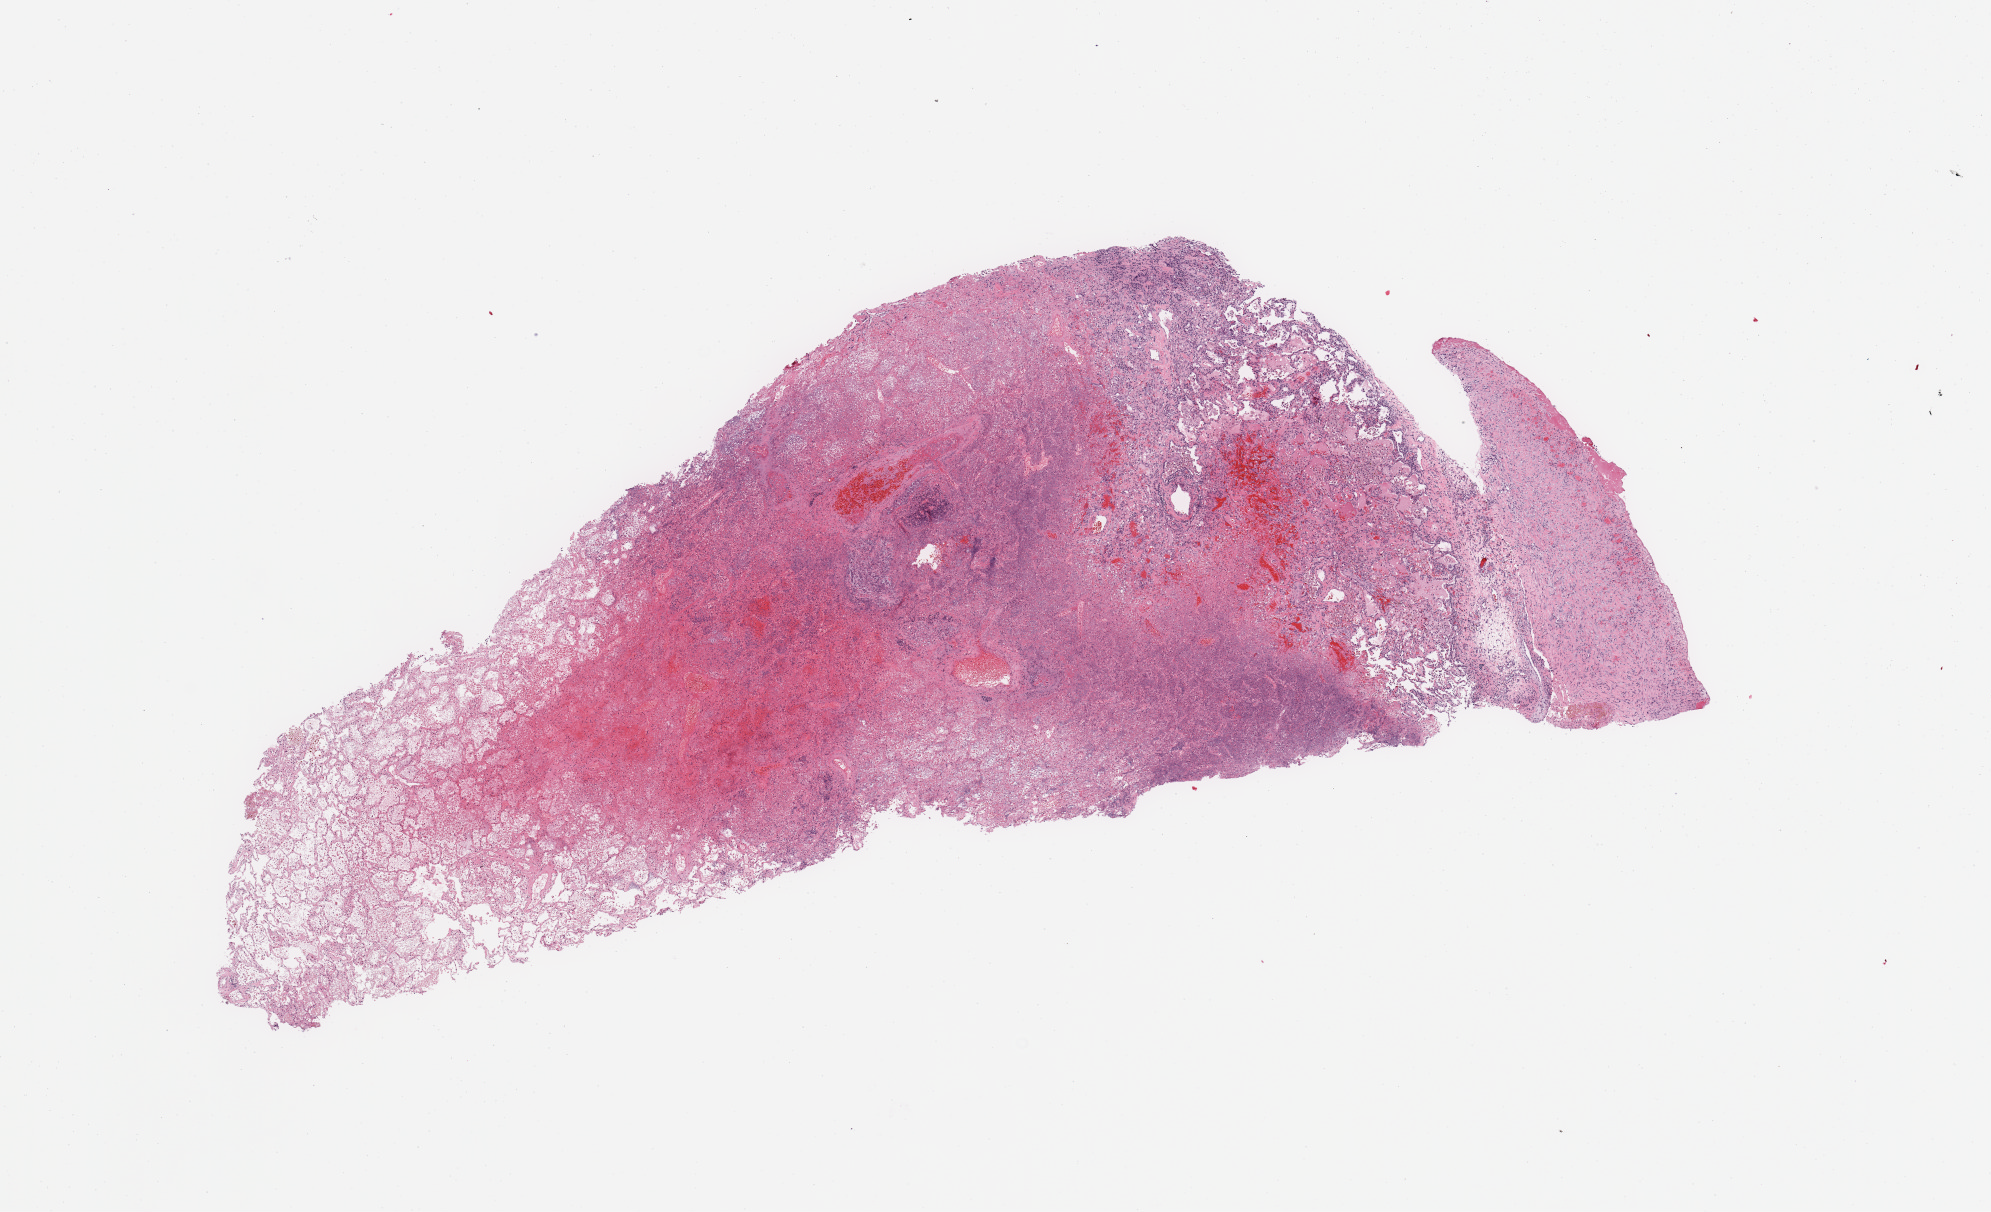
H&E-stained whole-slide image — whole scanned area (about 15.8 x 9.6 mm, slide scanned at 20x) shown as a low-resolution overview. Normal (non-tumour) tissue sample, lung. Patient: male, age 40 years.
• this section: normal (non-tumour) tissue from the same patient
• patient diagnosis: Squamous cell carcinoma, NOS